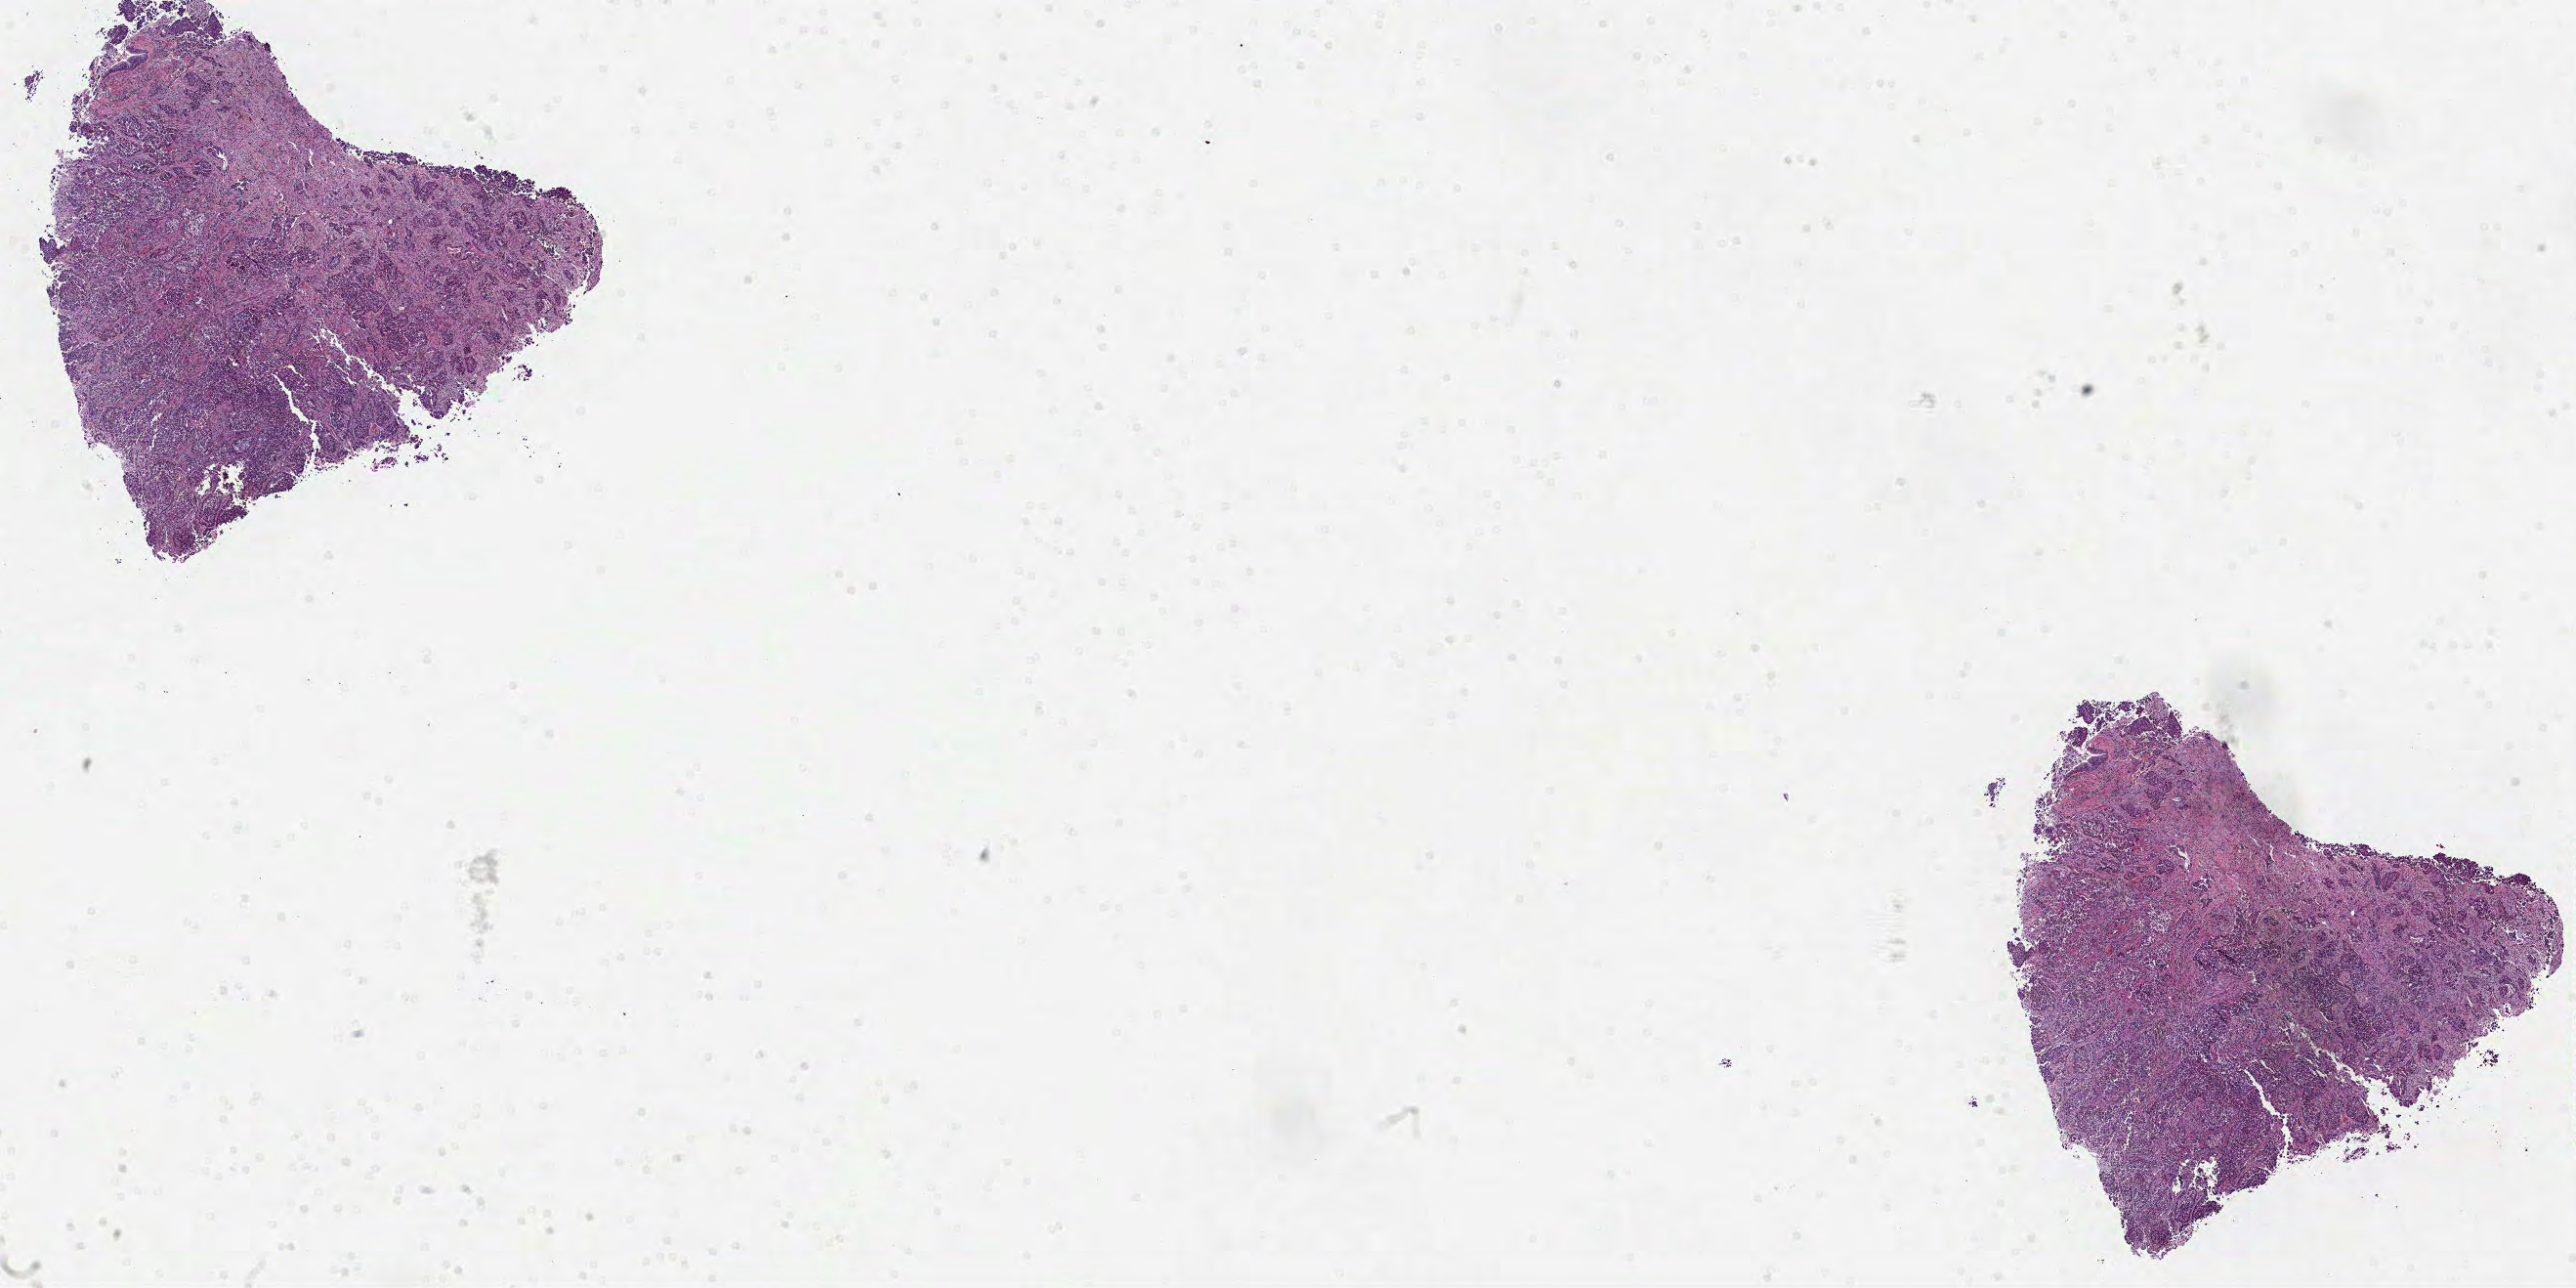
H&E-stained whole-slide image — shown as a low-resolution overview of the whole scanned area (about 21.3 x 10.6 mm). Formalin-fixed paraffin-embedded (FFPE) diagnostic section. Primary tumour sample from the lung. Patient: male, age at initial diagnosis 58 years.
• histologic diagnosis: Adenocarcinoma, NOS (upper lobe, lung)
• laterality: right
• AJCC pathologic stage: IA (7th edition)